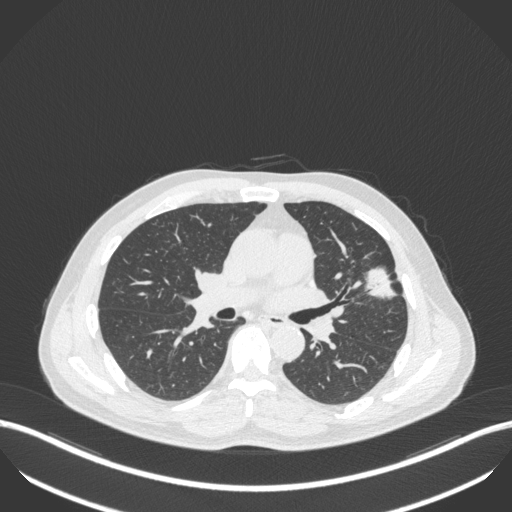
Chest CT, one axial slice; position 223 of 418 along the scan axis; reconstruction kernel B31f; lung window (W 1500 / L -600 HU); 512 × 512 image matrix. Patient: male, 55 years. From the clinical record (not read from this slice): clinical TNM (as recorded): T1c N0 M0; histopathological grade: G2-3.
Annotated regions visible in this slice (rectangle marked by the reading radiologist):
- lung tumour (recorded histology: adenocarcinoma): bounding box [x1, y1, x2, y2] px = [356, 267, 401, 302]